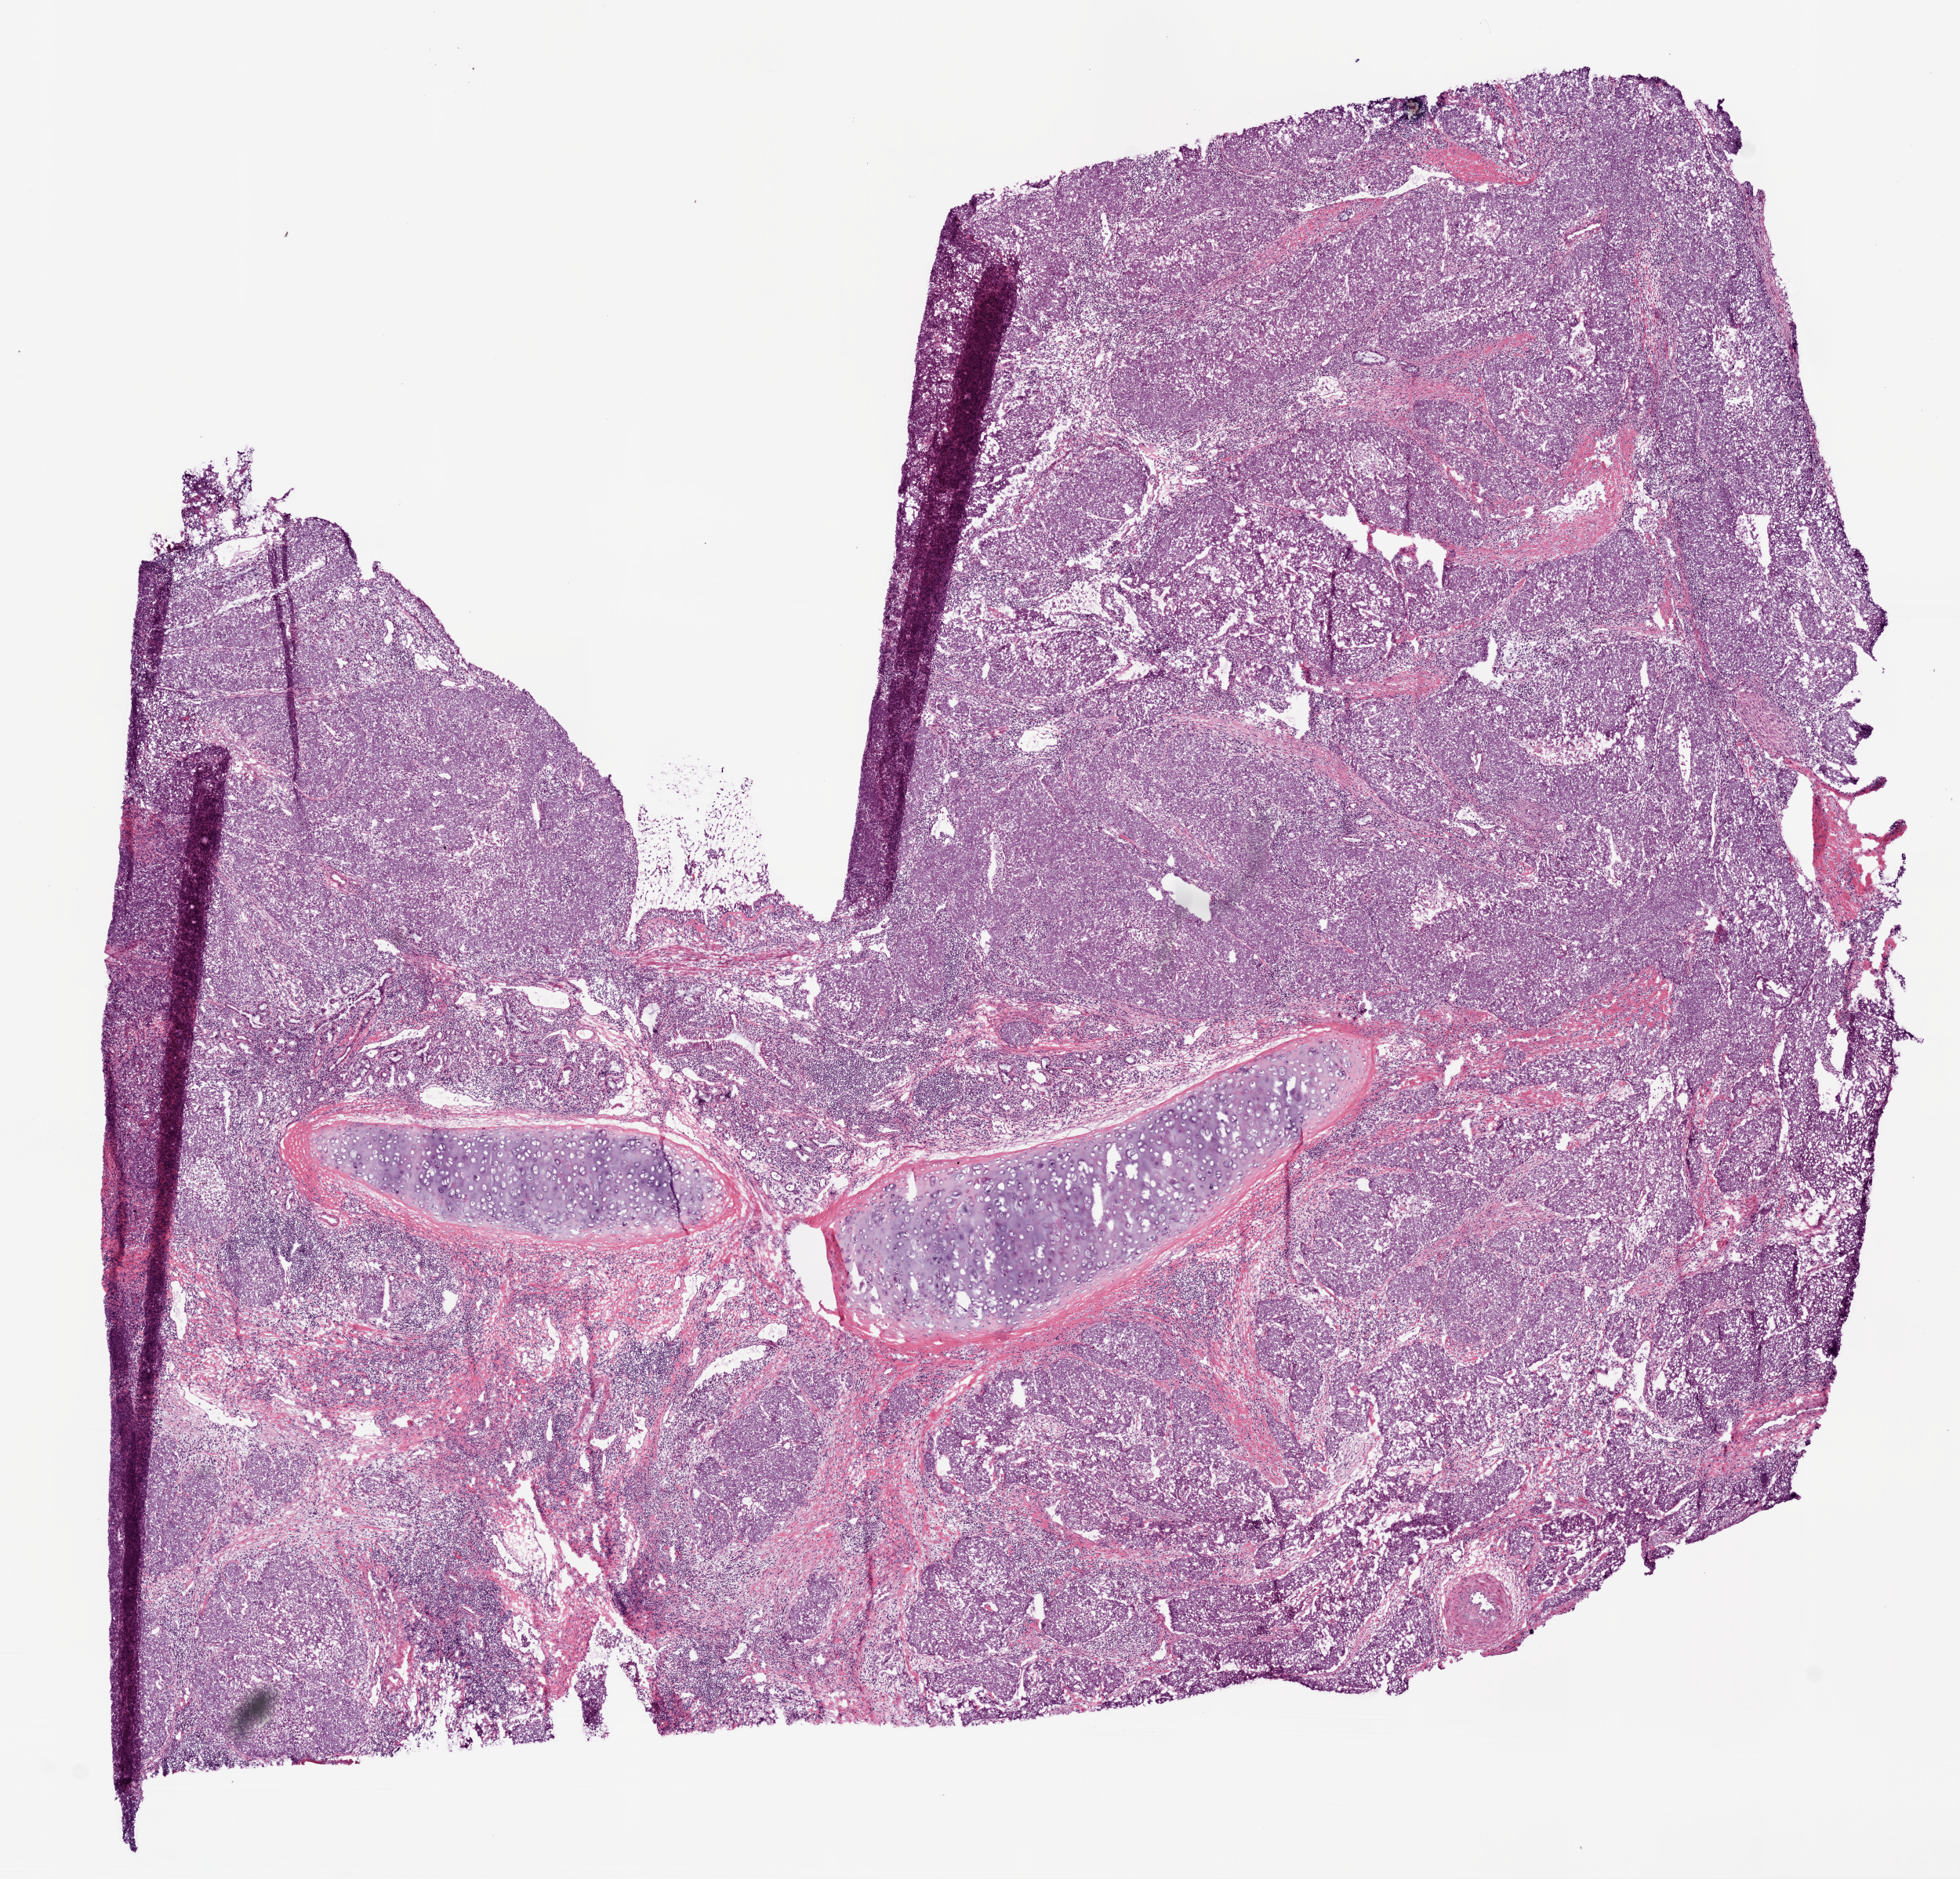
Whole-slide histology image, H&E-stained, low-resolution overview of the scanned area, about 10.0 x 9.6 mm. Frozen section from the bottom of the tissue portion. Primary tumour sample from the lung. Patient: male, age at initial diagnosis 53 years. Composition of this section per pathologist review: tumour cells 80%, tumour nuclei 75%, normal cells 5%, stromal cells 10%, necrosis 5%.
* histologic diagnosis: Adenocarcinoma, NOS (lower lobe, lung)
* laterality: right
* AJCC pathologic stage: IIIA (7th edition)